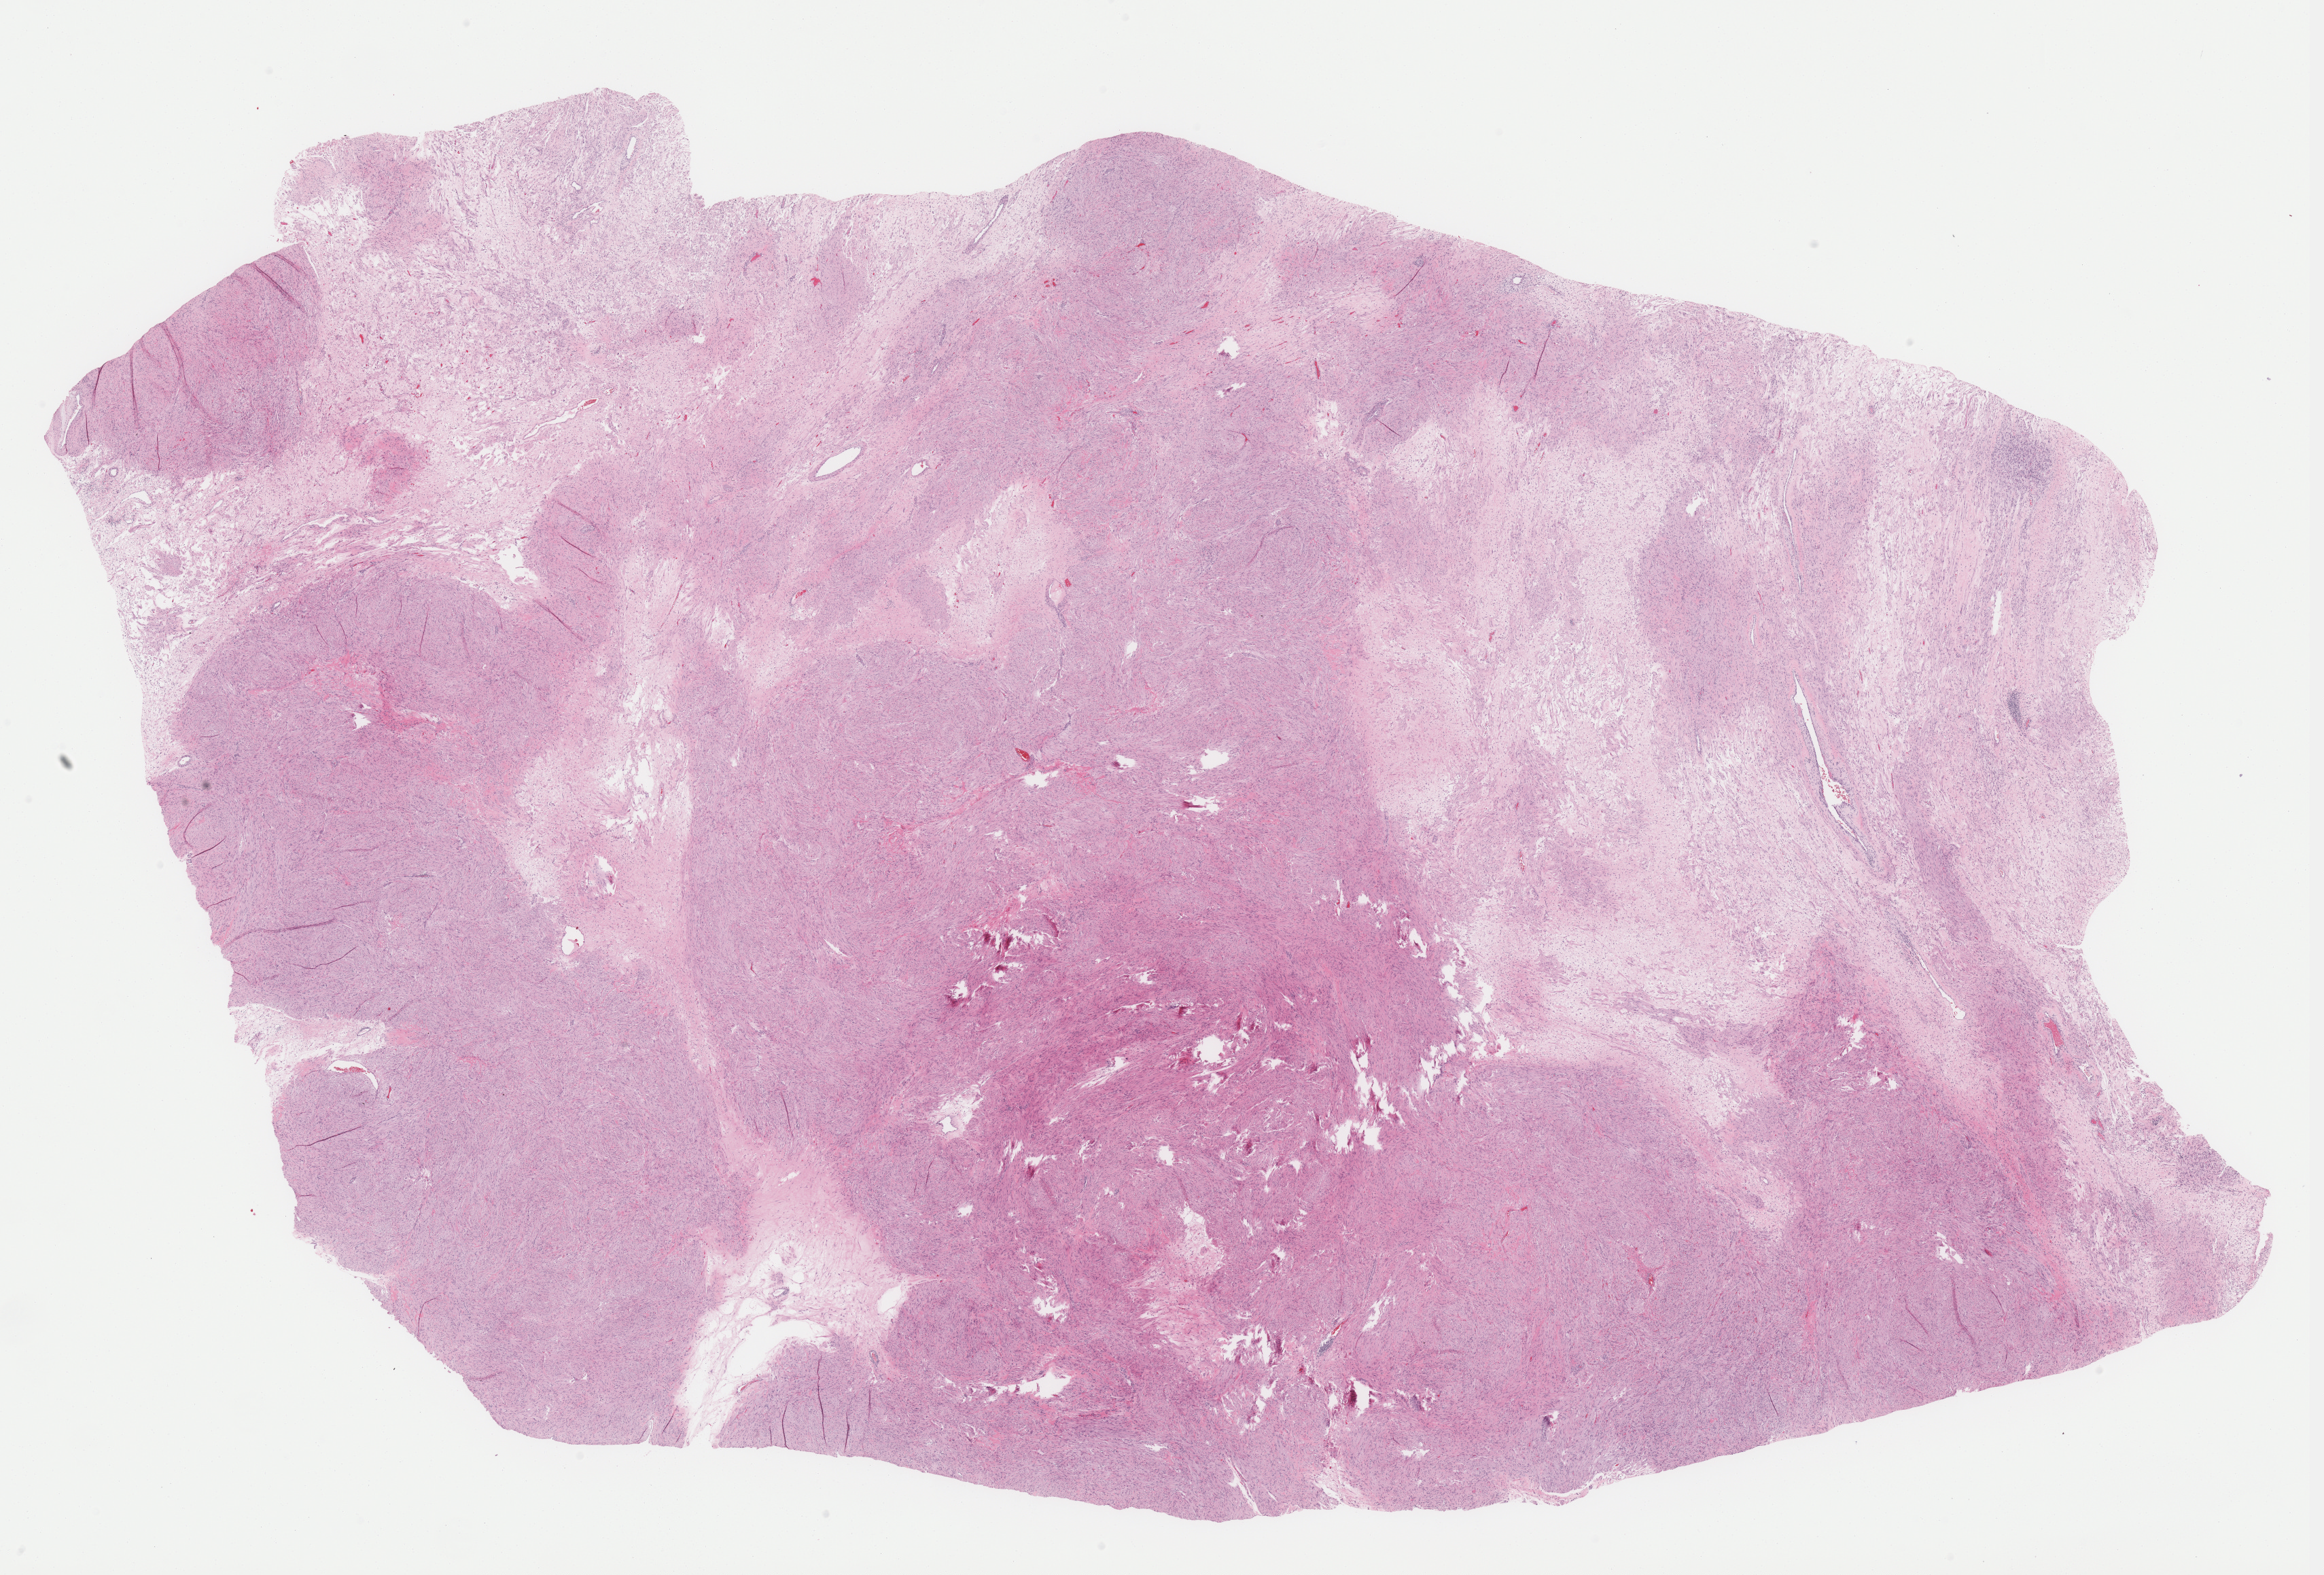
Whole-slide histology image, H&E-stained, a low-resolution overview of the entire scanned area, about 27.3 x 18.5 mm (slide scanned at 40x); formalin-fixed paraffin-embedded (FFPE) diagnostic section; connective, subcutaneous and other soft tissues, primary tumour sample. Female, age 45 years at initial diagnosis.
- histologic diagnosis: Leiomyosarcoma, NOS (overlapping lesion of connective, subcutaneous and other soft tissues)